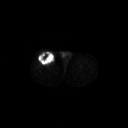
FDG PET of an extremity soft-tissue mass (from a PET/CT study), one axial slice; slice 282 of 311 in the series (ordered by position); 3.27 mm slice thickness; 128 × 128 image matrix. Patient: male, 56 years. From the clinical record (not read from this slice): histological type: pleiomorphic leiomyosarcoma; grade: intermediate; site of the primary tumour: right thigh.
Outlined on this slice (expert contour drawn on MRI and transferred to this co-registered scan by the dataset authors):
- gross tumour volume including surrounding oedema: box from (x=38, y=52) to (x=55, y=65) px
- gross tumour volume (mass): (x=38, y=52)–(x=55, y=65)